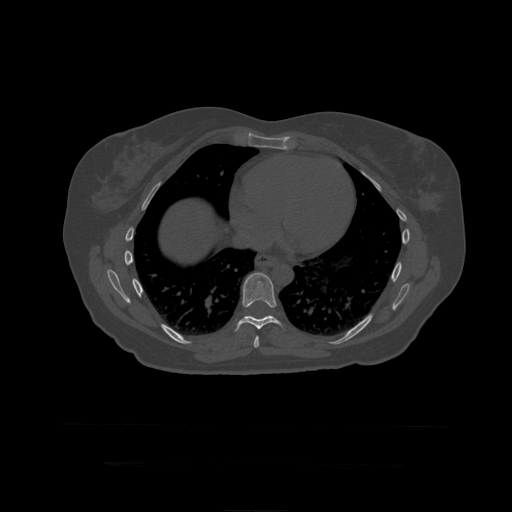
CT including the spine, one axial slice; slice 261 of 399 in the series (ordered by position); bone window (W 1800 / L 400 HU); 1.25 mm slice thickness; 512 × 512 image matrix. Patient age 41 years. Case-level facts recorded for this patient, not image findings: primary cancer: breast.
Annotated regions visible in this slice (semi-automatic segmentation, software-assisted and operator-edited):
- T8 vertebra: bounding box <254,336,259,348> (left, top, right, bottom; pixels)
- T9 vertebra: <235,273,283,332>